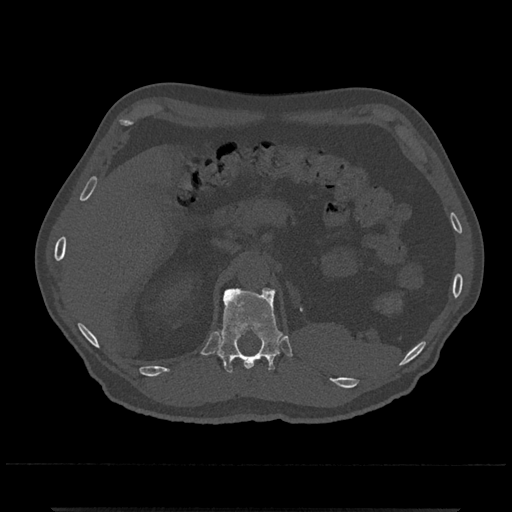
CT including the spine, one axial slice. Slice 435 of 797 in the series (ordered by position). Reconstruction kernel Br40s/3. 120 kVp. Bone window (W 1800 / L 400 HU). 512 × 512 image matrix. Patient: male, 67 years. Case-level facts recorded for this patient, not image findings: primary cancer: prostate.
Outlined on this slice (semi-automatically segmented with operator editing):
- T12 vertebra: bounding box [x1, y1, x2, y2] px = [216, 288, 282, 373]